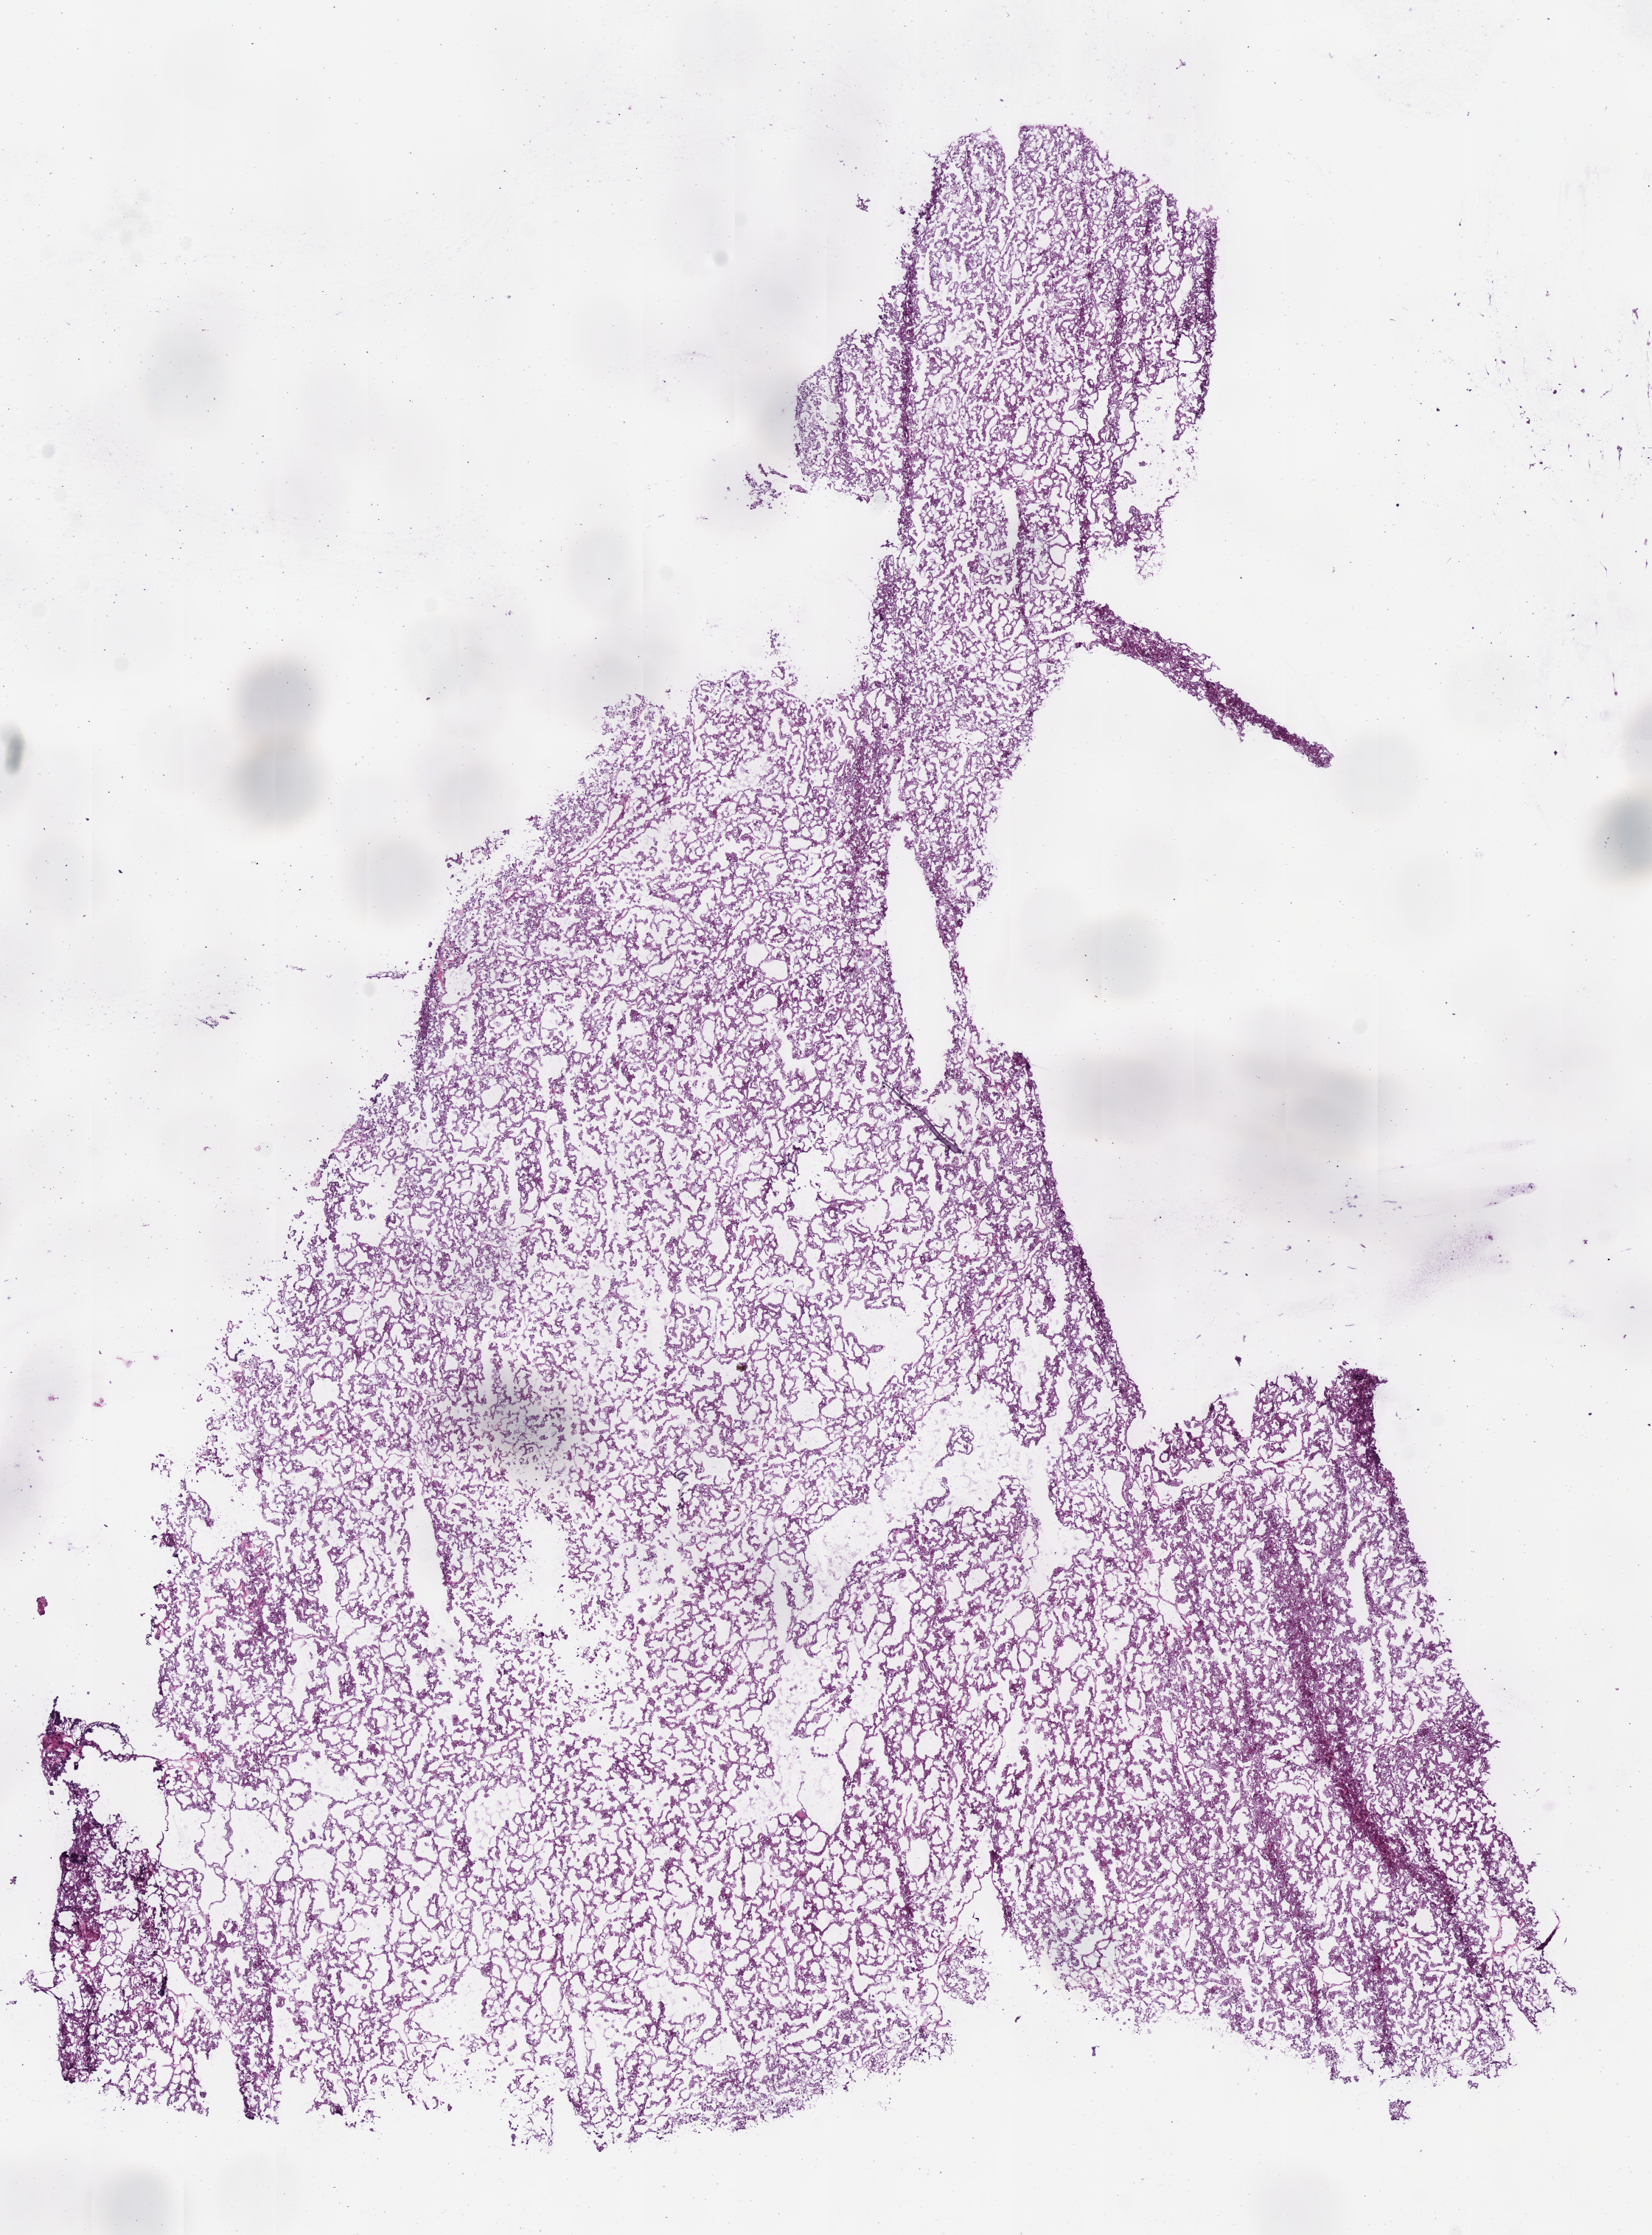
Whole-slide histology image, H&E-stained, low-resolution overview of the scanned area, about 8.8 x 11.9 mm. Frozen section from the bottom of the tissue portion. Sample: primary tumour, kidney. Female patient; age at initial diagnosis 45 years. Slide review estimates, as recorded: tumour cells 95%, tumour nuclei 95%, normal cells 0%, stromal cells 5%, necrosis 0%.
Lymph nodes positive (case pathology): 0 of 9 examined. Laterality: left. AJCC pathologic stage: II (6th edition). TNM: T2b N0 M0. Histologic diagnosis: Renal cell carcinoma, chromophobe type.